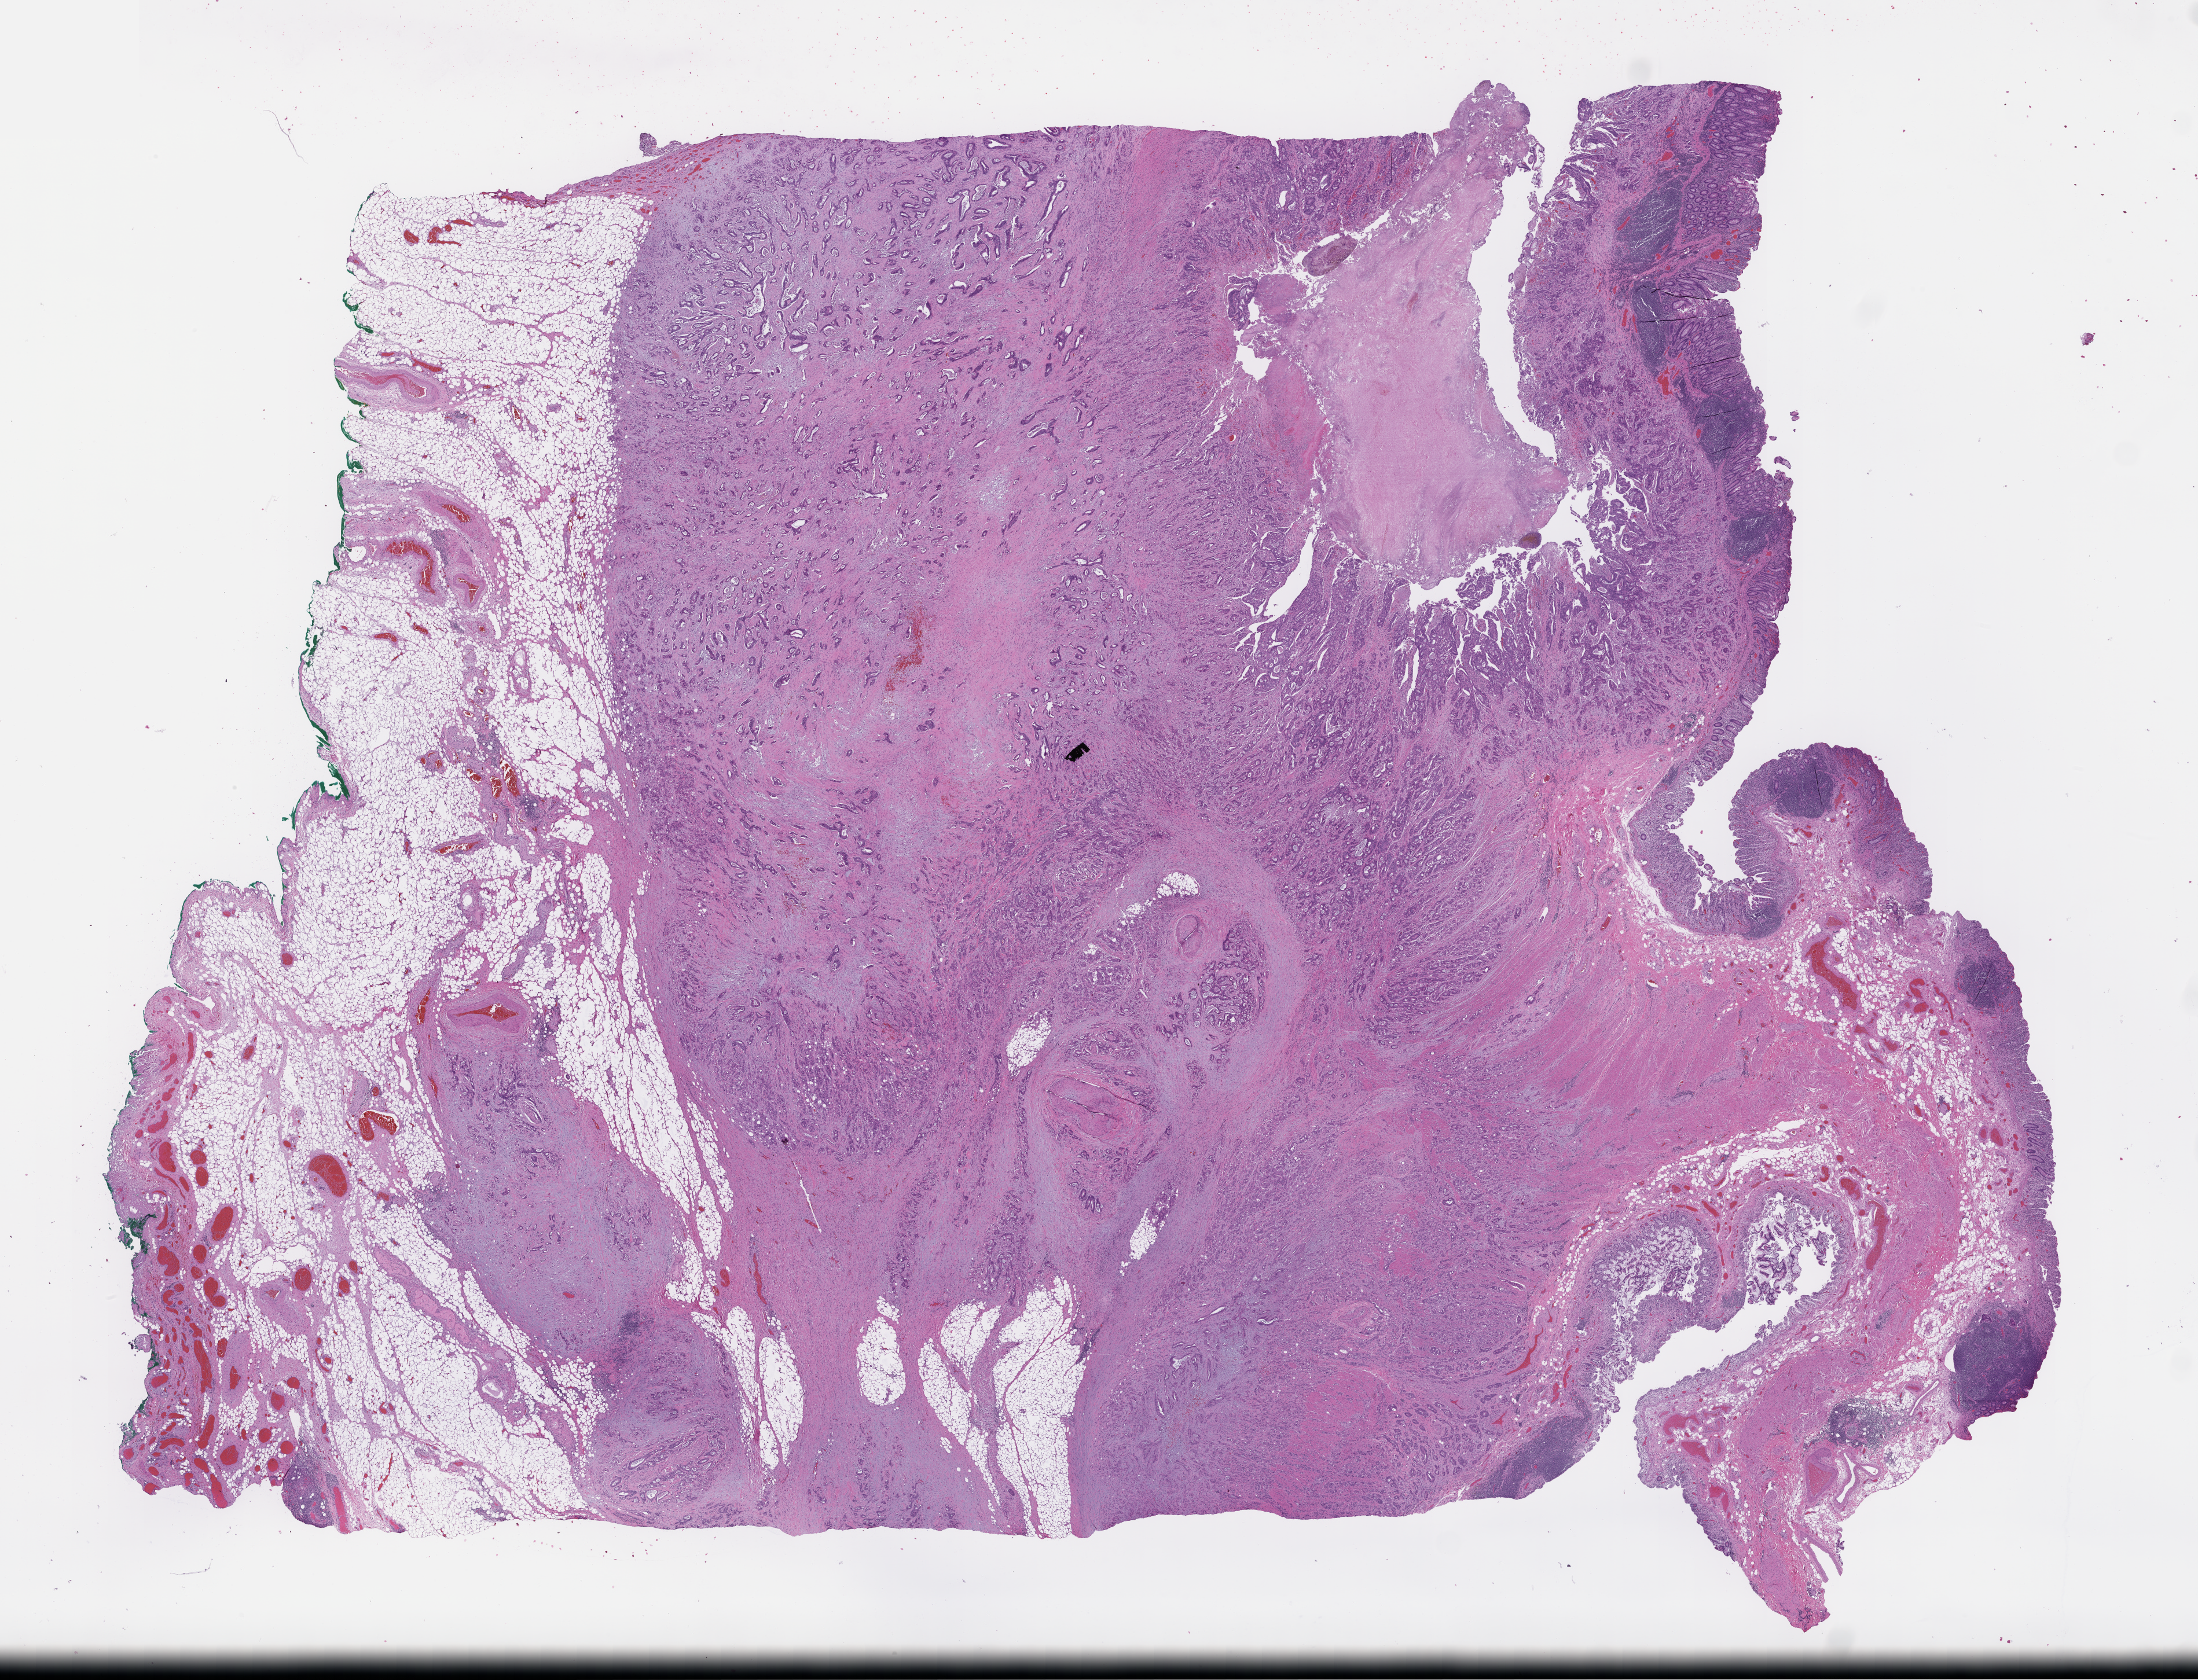
Whole-slide image, haematoxylin and eosin stain — a low-resolution overview of the entire scanned area, about 30.7 x 23.4 mm. Formalin-fixed paraffin-embedded section. Site: colon. Archival tissue. Patient sex: female.
This section: primary tumor. Diagnosis: Colorectal Carcinoma.